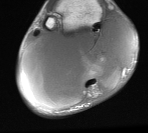
MRI of an extremity soft-tissue mass, one axial slice. Position 18 of 76 along the scan axis. MR volume resampled by the dataset authors to the PET/CT grid (not the native acquisition matrix). 3.27 mm slice thickness. 148 × 133 image matrix, field of view 145 × 130 mm. Male patient. Case-level facts recorded for this patient, not image findings: histological type: liposarcoma - round cell; grade: high; site of the primary tumour: right calf.
Outlined on this slice (expert contour drawn on MRI and transferred to this co-registered scan by the dataset authors):
- gross tumour volume (mass): bounding box (x1, y1, x2, y2) in pixels: (20, 17, 137, 111)